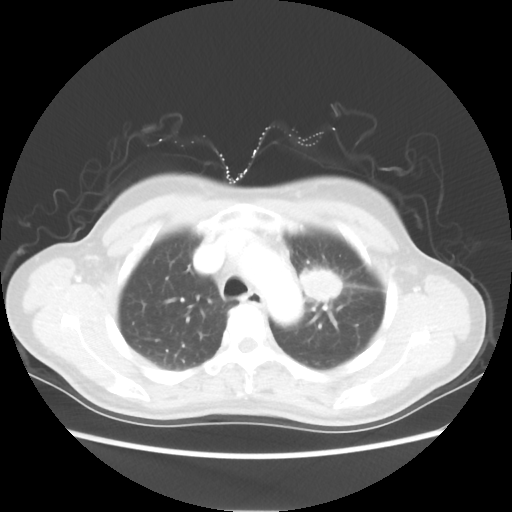
Chest CT, one axial slice. Slice 41 of 54 in the series (ordered by position). Reconstruction kernel STANDARD. Lung window (W 1500 / L -600 HU). 5 mm slice thickness. 512 × 512 image matrix, field of view 360 × 360 mm. Female patient, age 53 years. From the clinical record (not read from this slice): clinical TNM (as recorded): T1c N0 M0.
Outlined on this slice (bounding box drawn by a radiologist):
- lung tumour (recorded histology: adenocarcinoma): bounding box (x1, y1, x2, y2) in pixels: (295, 256, 350, 315)
- lung tumour (recorded histology: adenocarcinoma): (301, 262, 342, 302)